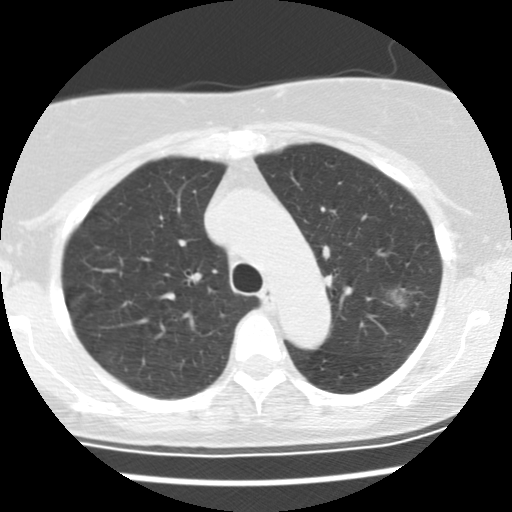
Low-dose screening chest CT, one axial slice; slice 102 of 137 in the series (ordered by position); reconstruction kernel STANDARD; 120 kVp; lung window (W 1500 / L -600 HU); 2.5 mm slice thickness; 512 × 512 image matrix, field of view 288 × 288 mm.
Structures marked on this image (expert manual segmentation):
- lesion 1 (tumor, upper lobe of left lung): box from (x=391, y=291) to (x=405, y=307) px